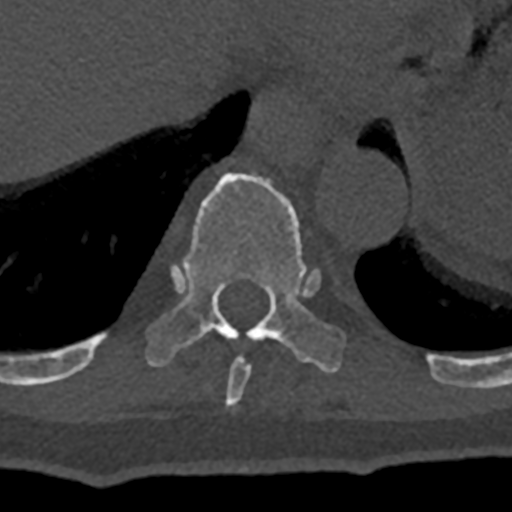
CT including the spine, one axial slice. 120 kVp. Bone window (W 1800 / L 400 HU). 0.5 mm slice thickness. 512 × 512 image matrix, field of view 160 × 160 mm. Patient: male, 74 years. From the clinical record (not read from this slice): primary cancer: renal.
Structures marked on this image (semi-automatic segmentation, software-assisted and operator-edited):
- T10 vertebra: bounding box [x1, y1, x2, y2] px = [70, 173, 432, 376]
- T9 vertebra: [225, 356, 251, 409]